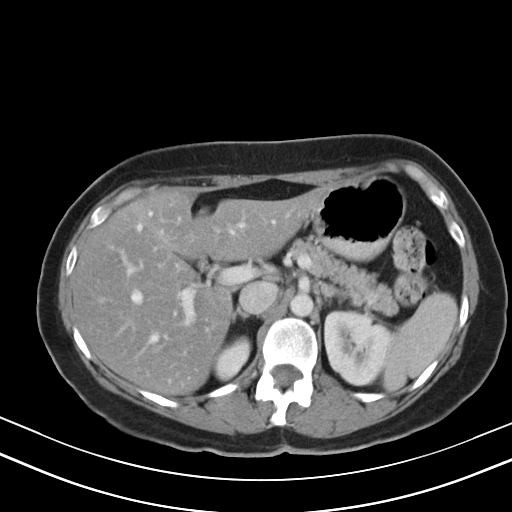
Contrast-enhanced abdominal CT, one axial slice. Position 29 of 47 along the scan axis. Reconstruction kernel B40s. 130 kVp. Intravenous contrast given. Soft-tissue window (W 400 / L 40 HU). 5 mm slice thickness. 512 × 512 image matrix. Female patient. From the clinical record (not read from this slice): diagnosis: colorectal cancer liver metastases, imaged before liver resection; multiple liver metastases: no; largest metastasis: 3.5 cm; disease in both lobes: no.
Structures marked on this image (outlined manually by an expert reader):
- hepatic veins: bounding box [x1, y1, x2, y2] px = [128, 212, 273, 341]
- liver: [74, 191, 319, 395]
- planned liver remnant (the part of the liver to remain after resection): [74, 192, 319, 395]
- portal vein (with intrahepatic branches): [123, 254, 195, 326]